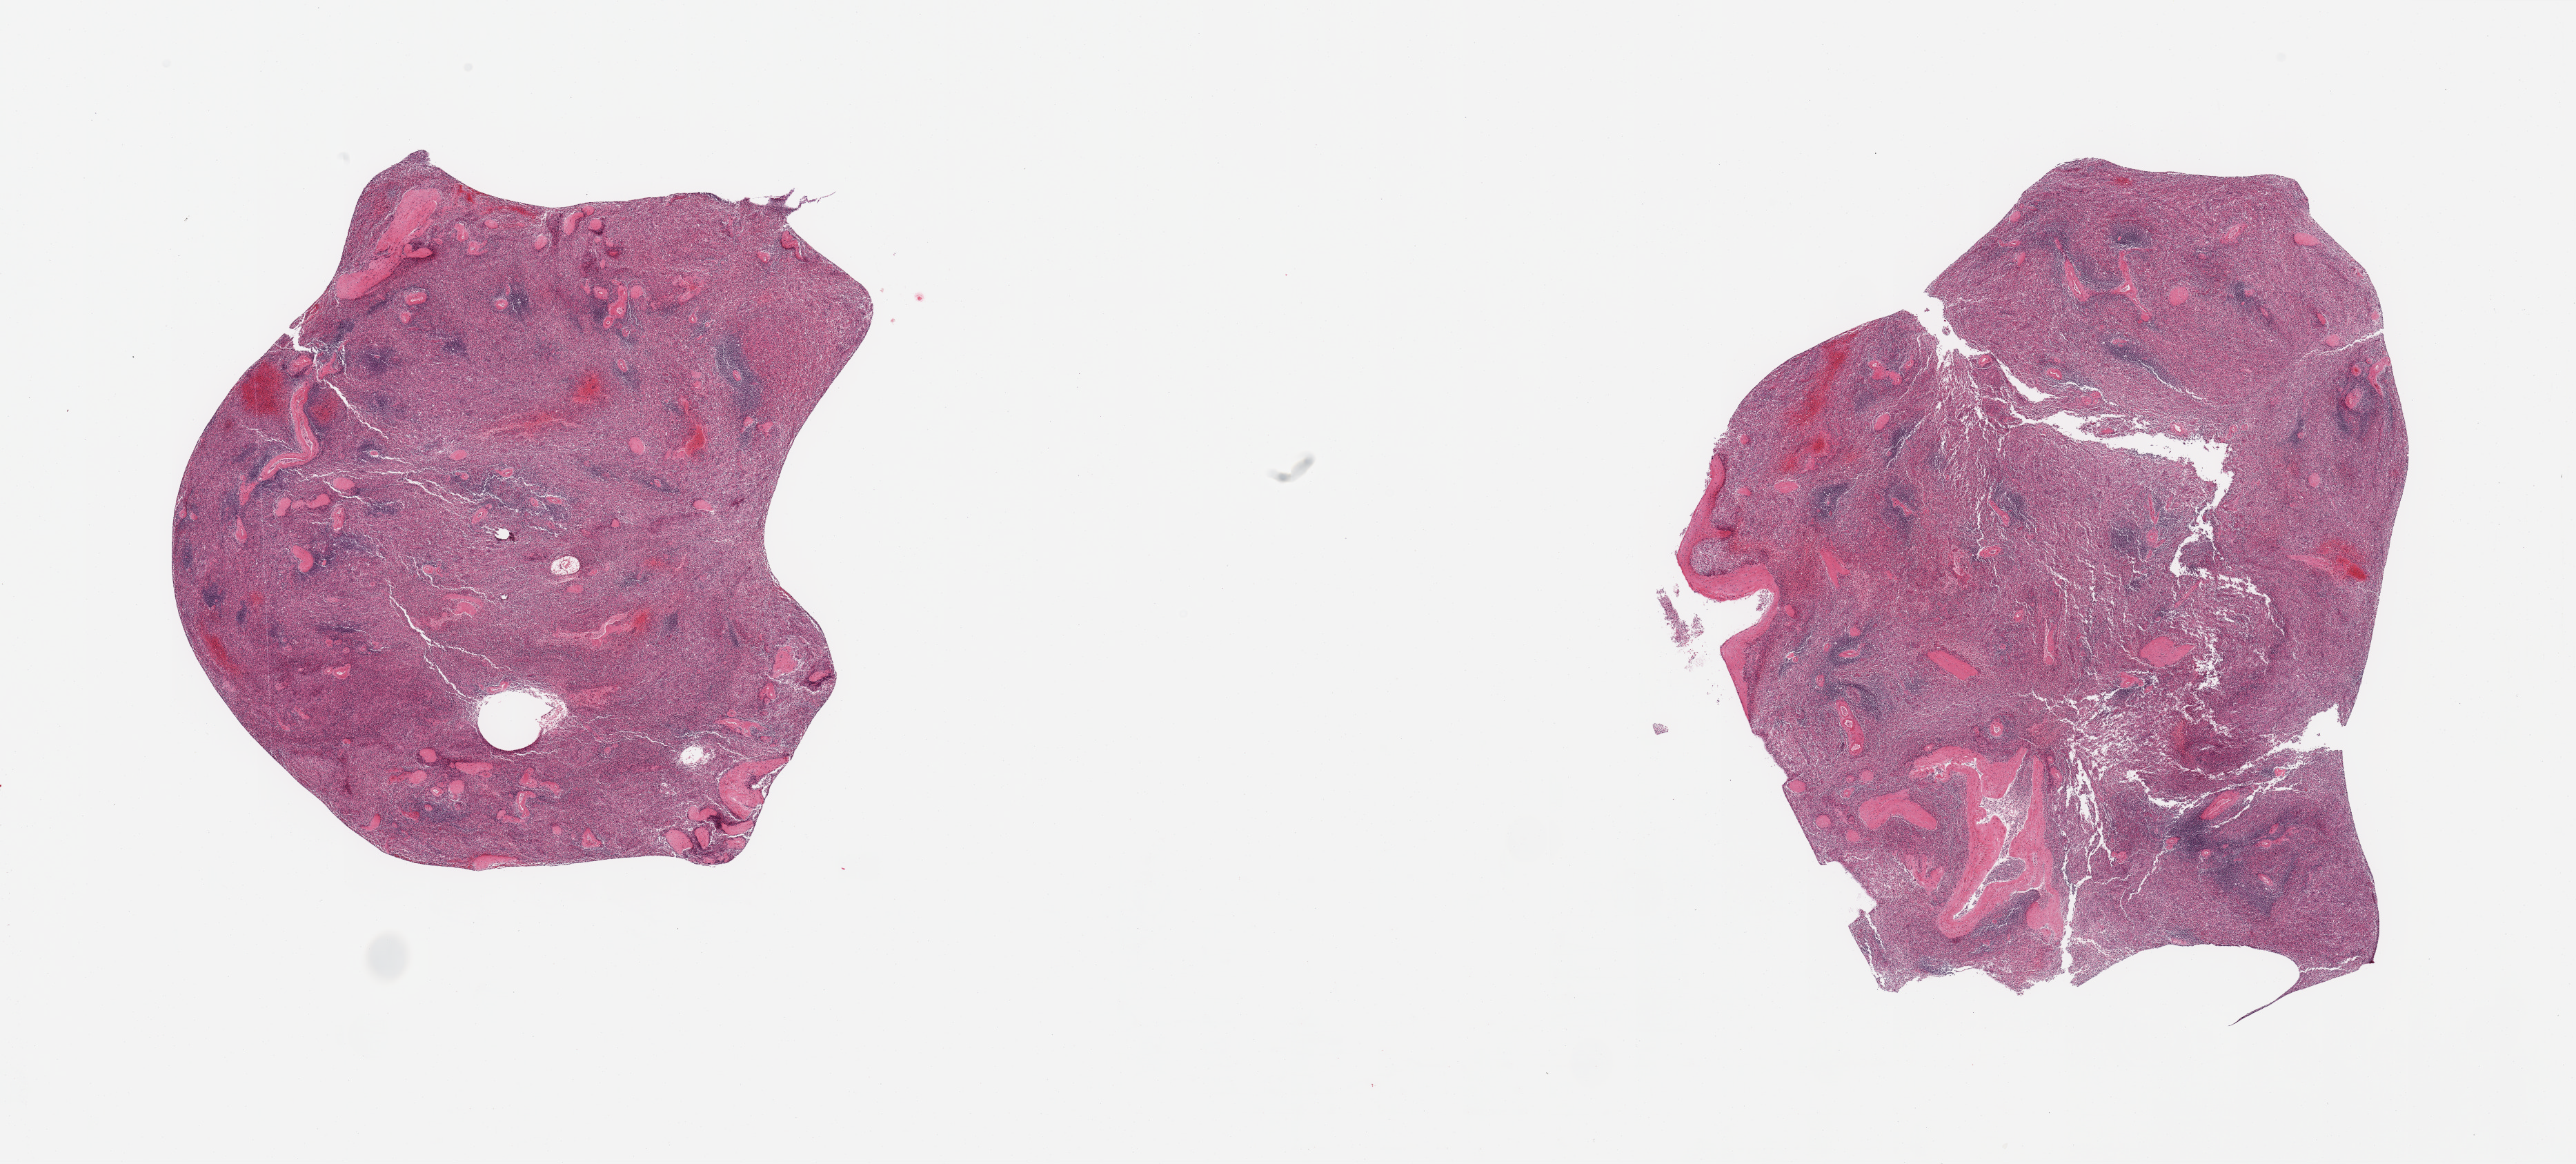
Digitized haematoxylin and eosin-stained section, a low-resolution overview of the entire scanned area, about 29.5 x 13.3 mm (acquisition: 20x scan). PAXgene-fixed paraffin-embedded (PFPE) section. Sampled site (target tissue): spleen. Donor tissue sample. Donor sex: male.
Review note (as recorded): 2 pieces, moderate congestion.